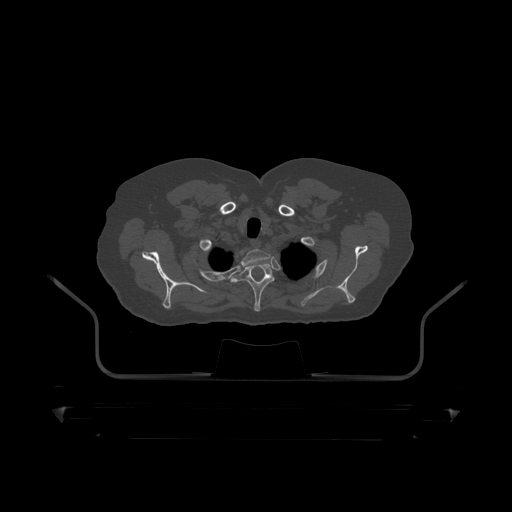
CT including the spine, one axial slice. 120 kVp. Bone window (W 1800 / L 400 HU). 512 × 512 image matrix, field of view 650 × 650 mm. Male patient, age 60 years. From the clinical record (not read from this slice): primary cancer: prostate.
Outlined on this slice (semi-automatically segmented with operator editing):
- T1 vertebra: box from (x=240, y=250) to (x=271, y=267) px
- T2 vertebra: (x=231, y=262)–(x=275, y=312)